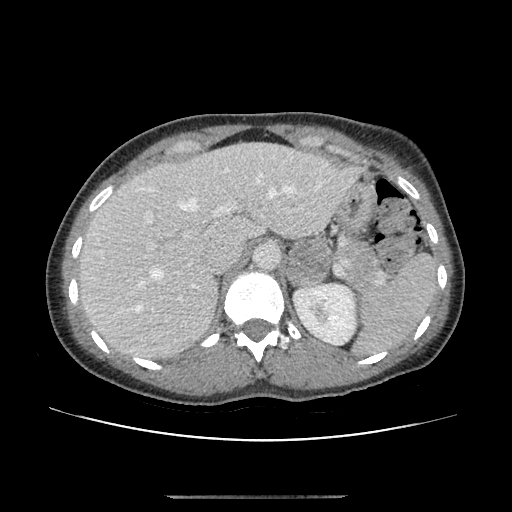
Contrast-enhanced abdominal CT, one axial slice. Slice 75 of 179 in the series (ordered by position). Reconstruction kernel STANDARD. 120 kVp. Soft-tissue window (W 400 / L 40 HU). 512 × 512 image matrix, field of view 360 × 360 mm. Patient: female, 51 years. Case-level facts recorded for this patient, not image findings: diagnosis: adrenocortical carcinoma; tumour side: left adrenal; tumour size at pathology: 3.5 cm; Ki-67 index: 45 %; stage (as recorded): 1.
Structures marked on this image (semi-automatically segmented with operator editing):
- mass: bounding box [x1, y1, x2, y2] px = [287, 239, 328, 285]